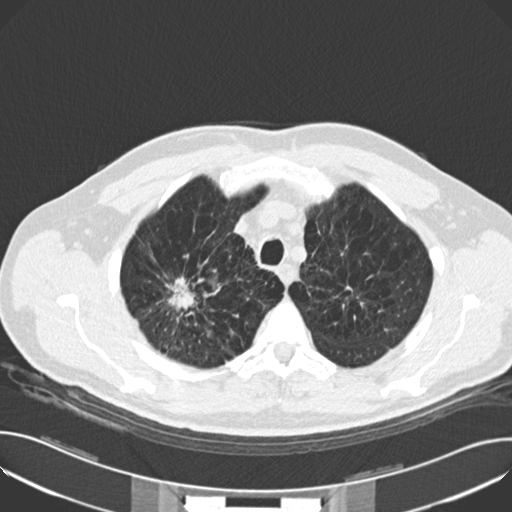
Low-dose screening chest CT, one axial slice. Slice 133 of 159 in the series (ordered by position). Reconstruction kernel B30f. 120 kVp. Lung window (W 1500 / L -600 HU). 2 mm slice thickness. 512 × 512 image matrix, field of view 380 × 380 mm.
Outlined on this slice (expert manual segmentation):
- lesion 1 (tumor, upper lobe of right lung): bounding box (x1, y1, x2, y2) in pixels: (167, 276, 195, 310)